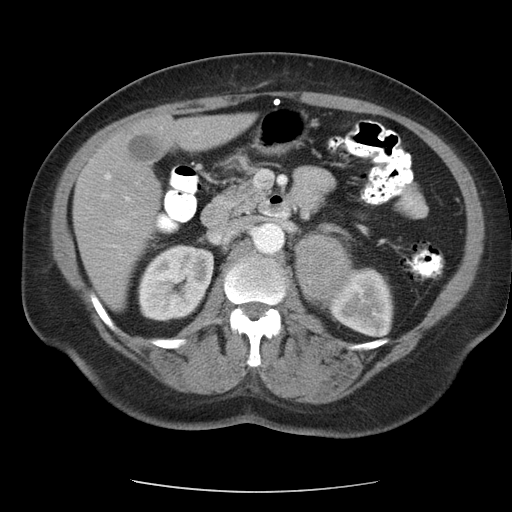
Contrast-enhanced abdominal CT, one axial slice; slice 62 of 95 in the series (ordered by position); reconstruction kernel STANDARD; 120 kVp; intravenous contrast given; soft-tissue window (W 400 / L 40 HU); 512 × 512 image matrix, field of view 362 × 362 mm. Female patient, age 71 years. From the clinical record (not read from this slice): diagnosis: adrenocortical carcinoma; tumour side: left adrenal; tumour size at pathology: 8.8 cm; Ki-67 index: 20 %; stage (as recorded): 2.
Annotated regions visible in this slice (semi-automatic segmentation, software-assisted and operator-edited):
- mass: box from (x=294, y=235) to (x=351, y=303) px